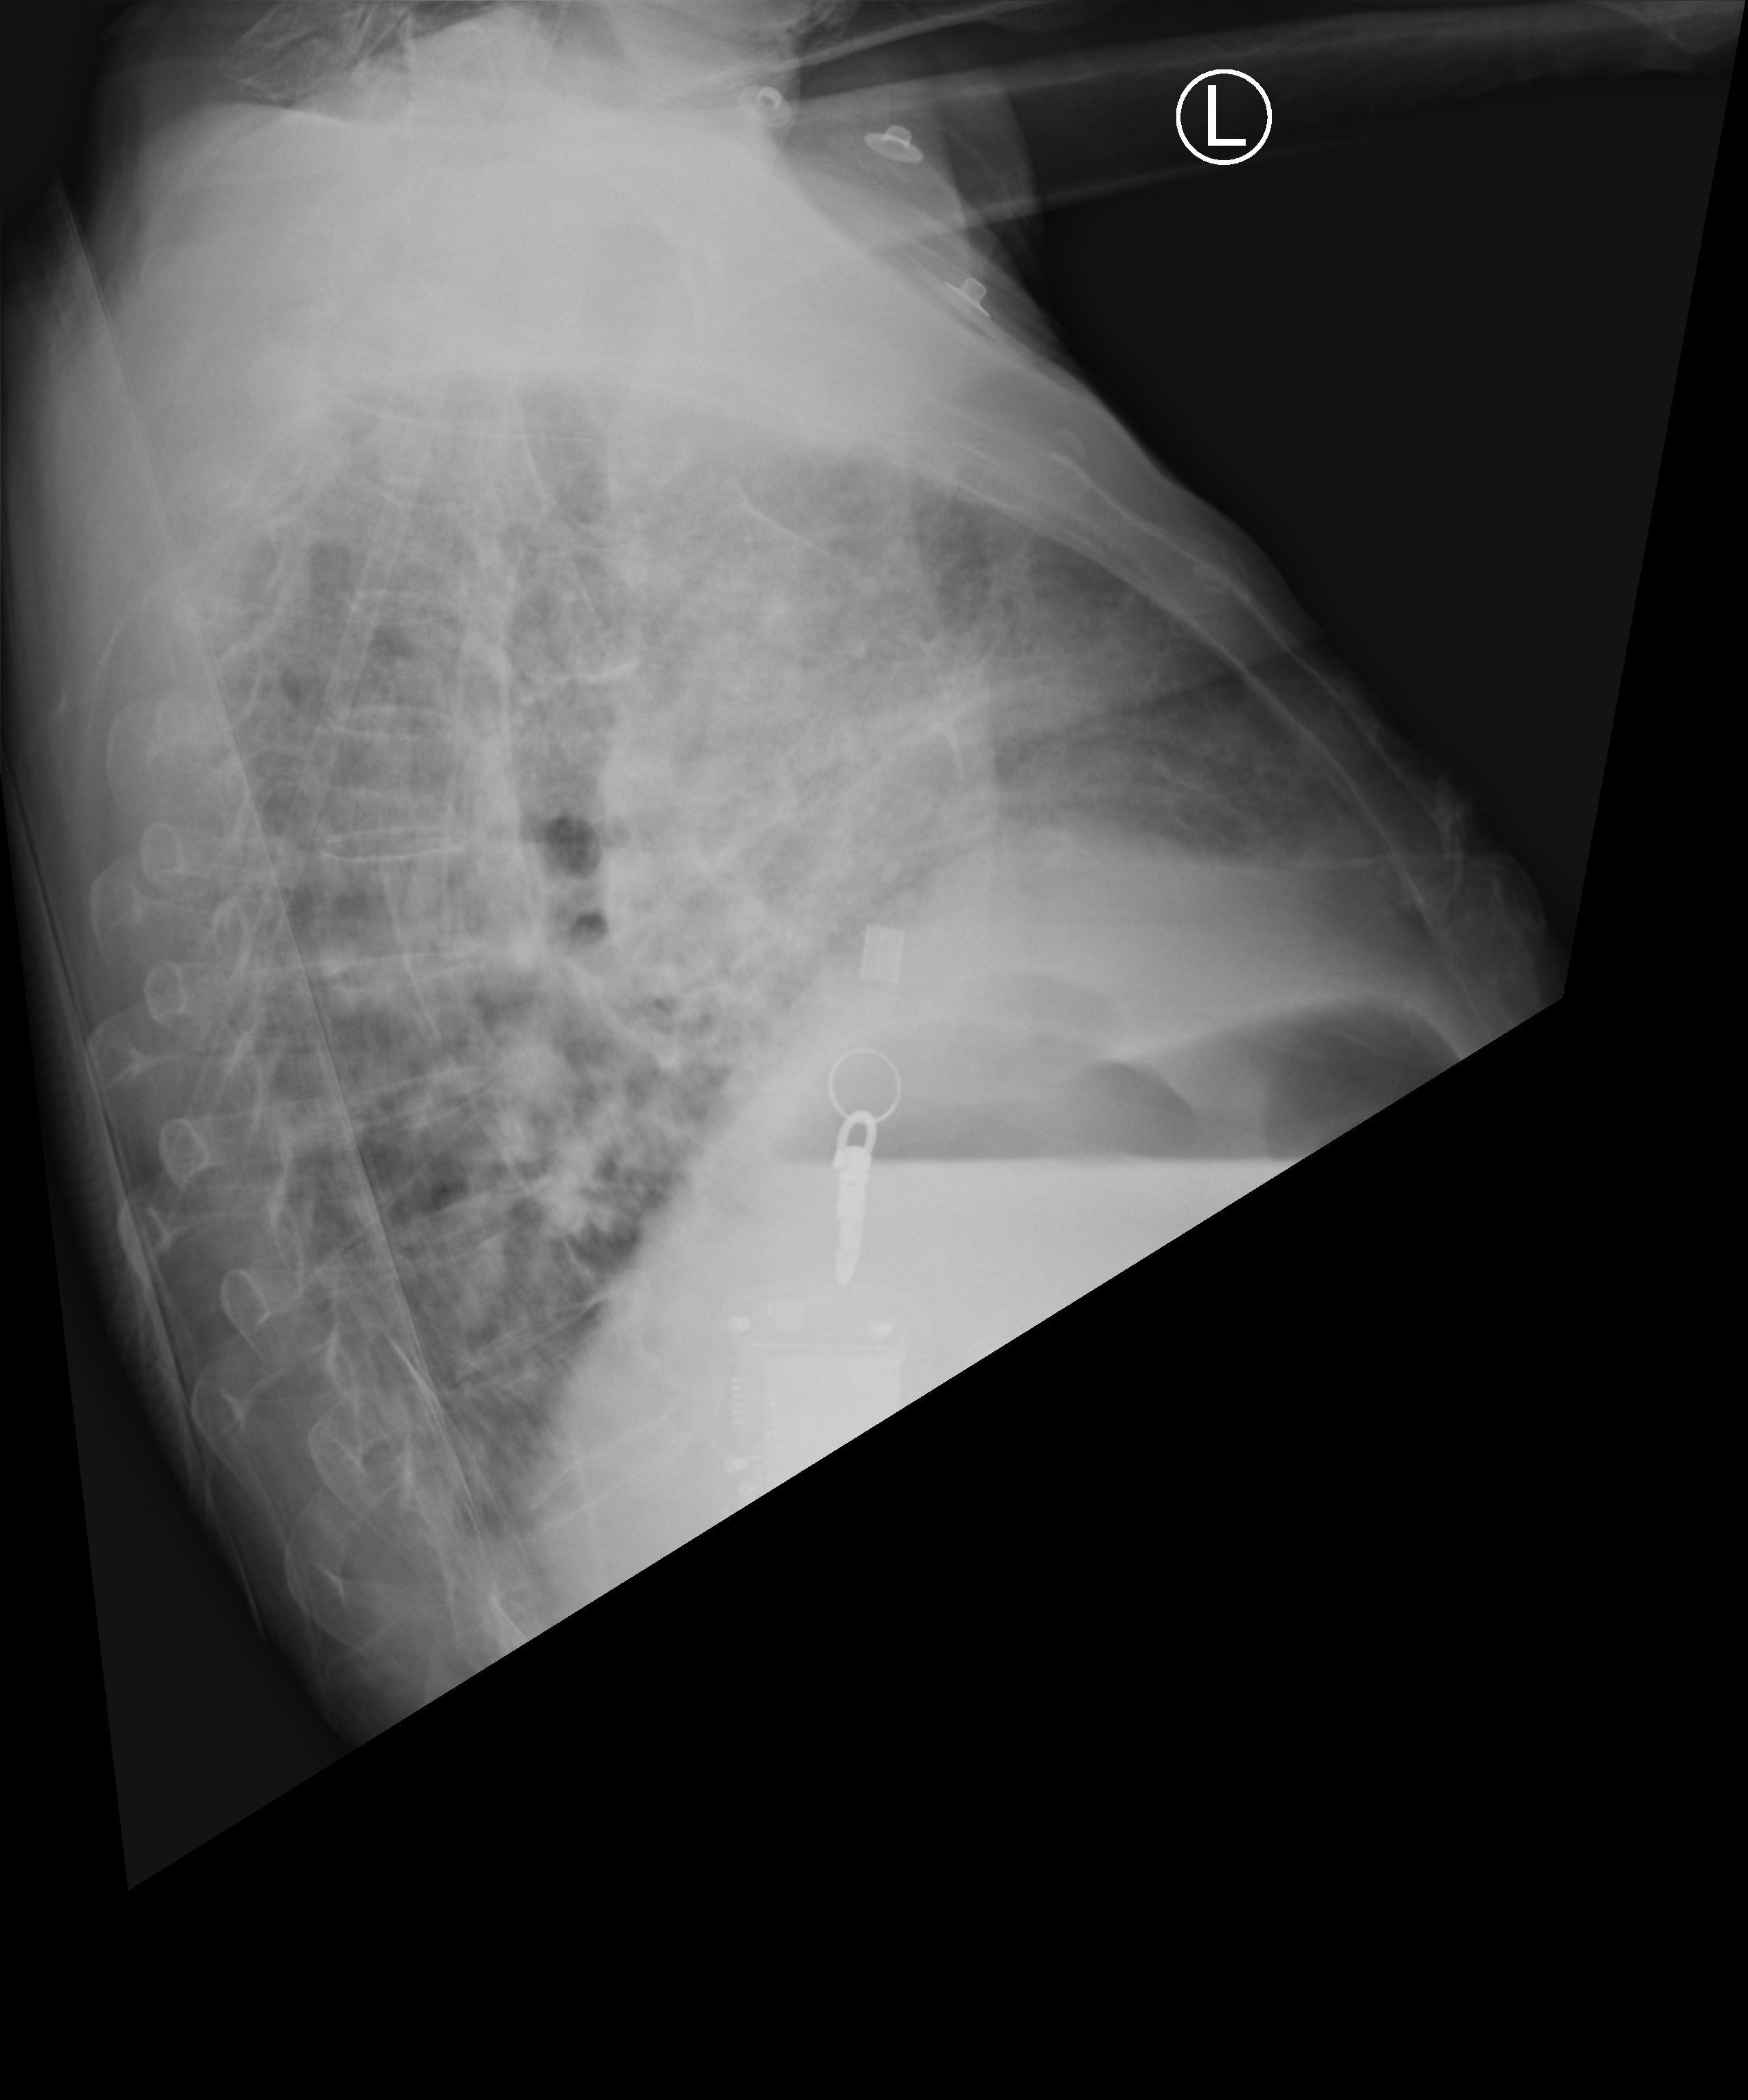
Chest X-ray. Patient hospitalised with COVID-19; male, aged 60–74 years.
Admission-level facts for this patient (not findings on this image; timing relative to this image not recorded):
- length of hospital stay: 20 days
- mechanically ventilated during this hospital stay: no